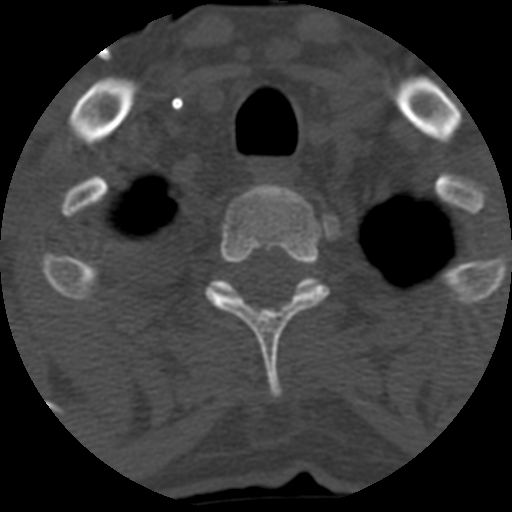
CT including the spine, one axial slice. Slice 502 of 708 in the series (ordered by position). One of 3 acquisitions stored at this slice position. Bone window (W 1800 / L 400 HU). 1.25 mm slice thickness. 512 × 512 image matrix, field of view 160 × 160 mm. Patient age 55 years. Case-level facts recorded for this patient, not image findings: primary cancer: colon; vertebrae with lytic lesions (as recorded): T12, L1, L5.
Annotated regions visible in this slice (semi-automatic segmentation, software-assisted and operator-edited):
- T2 vertebra: bounding box [x1, y1, x2, y2] px = [206, 183, 328, 399]
- T3 vertebra: [209, 279, 314, 298]